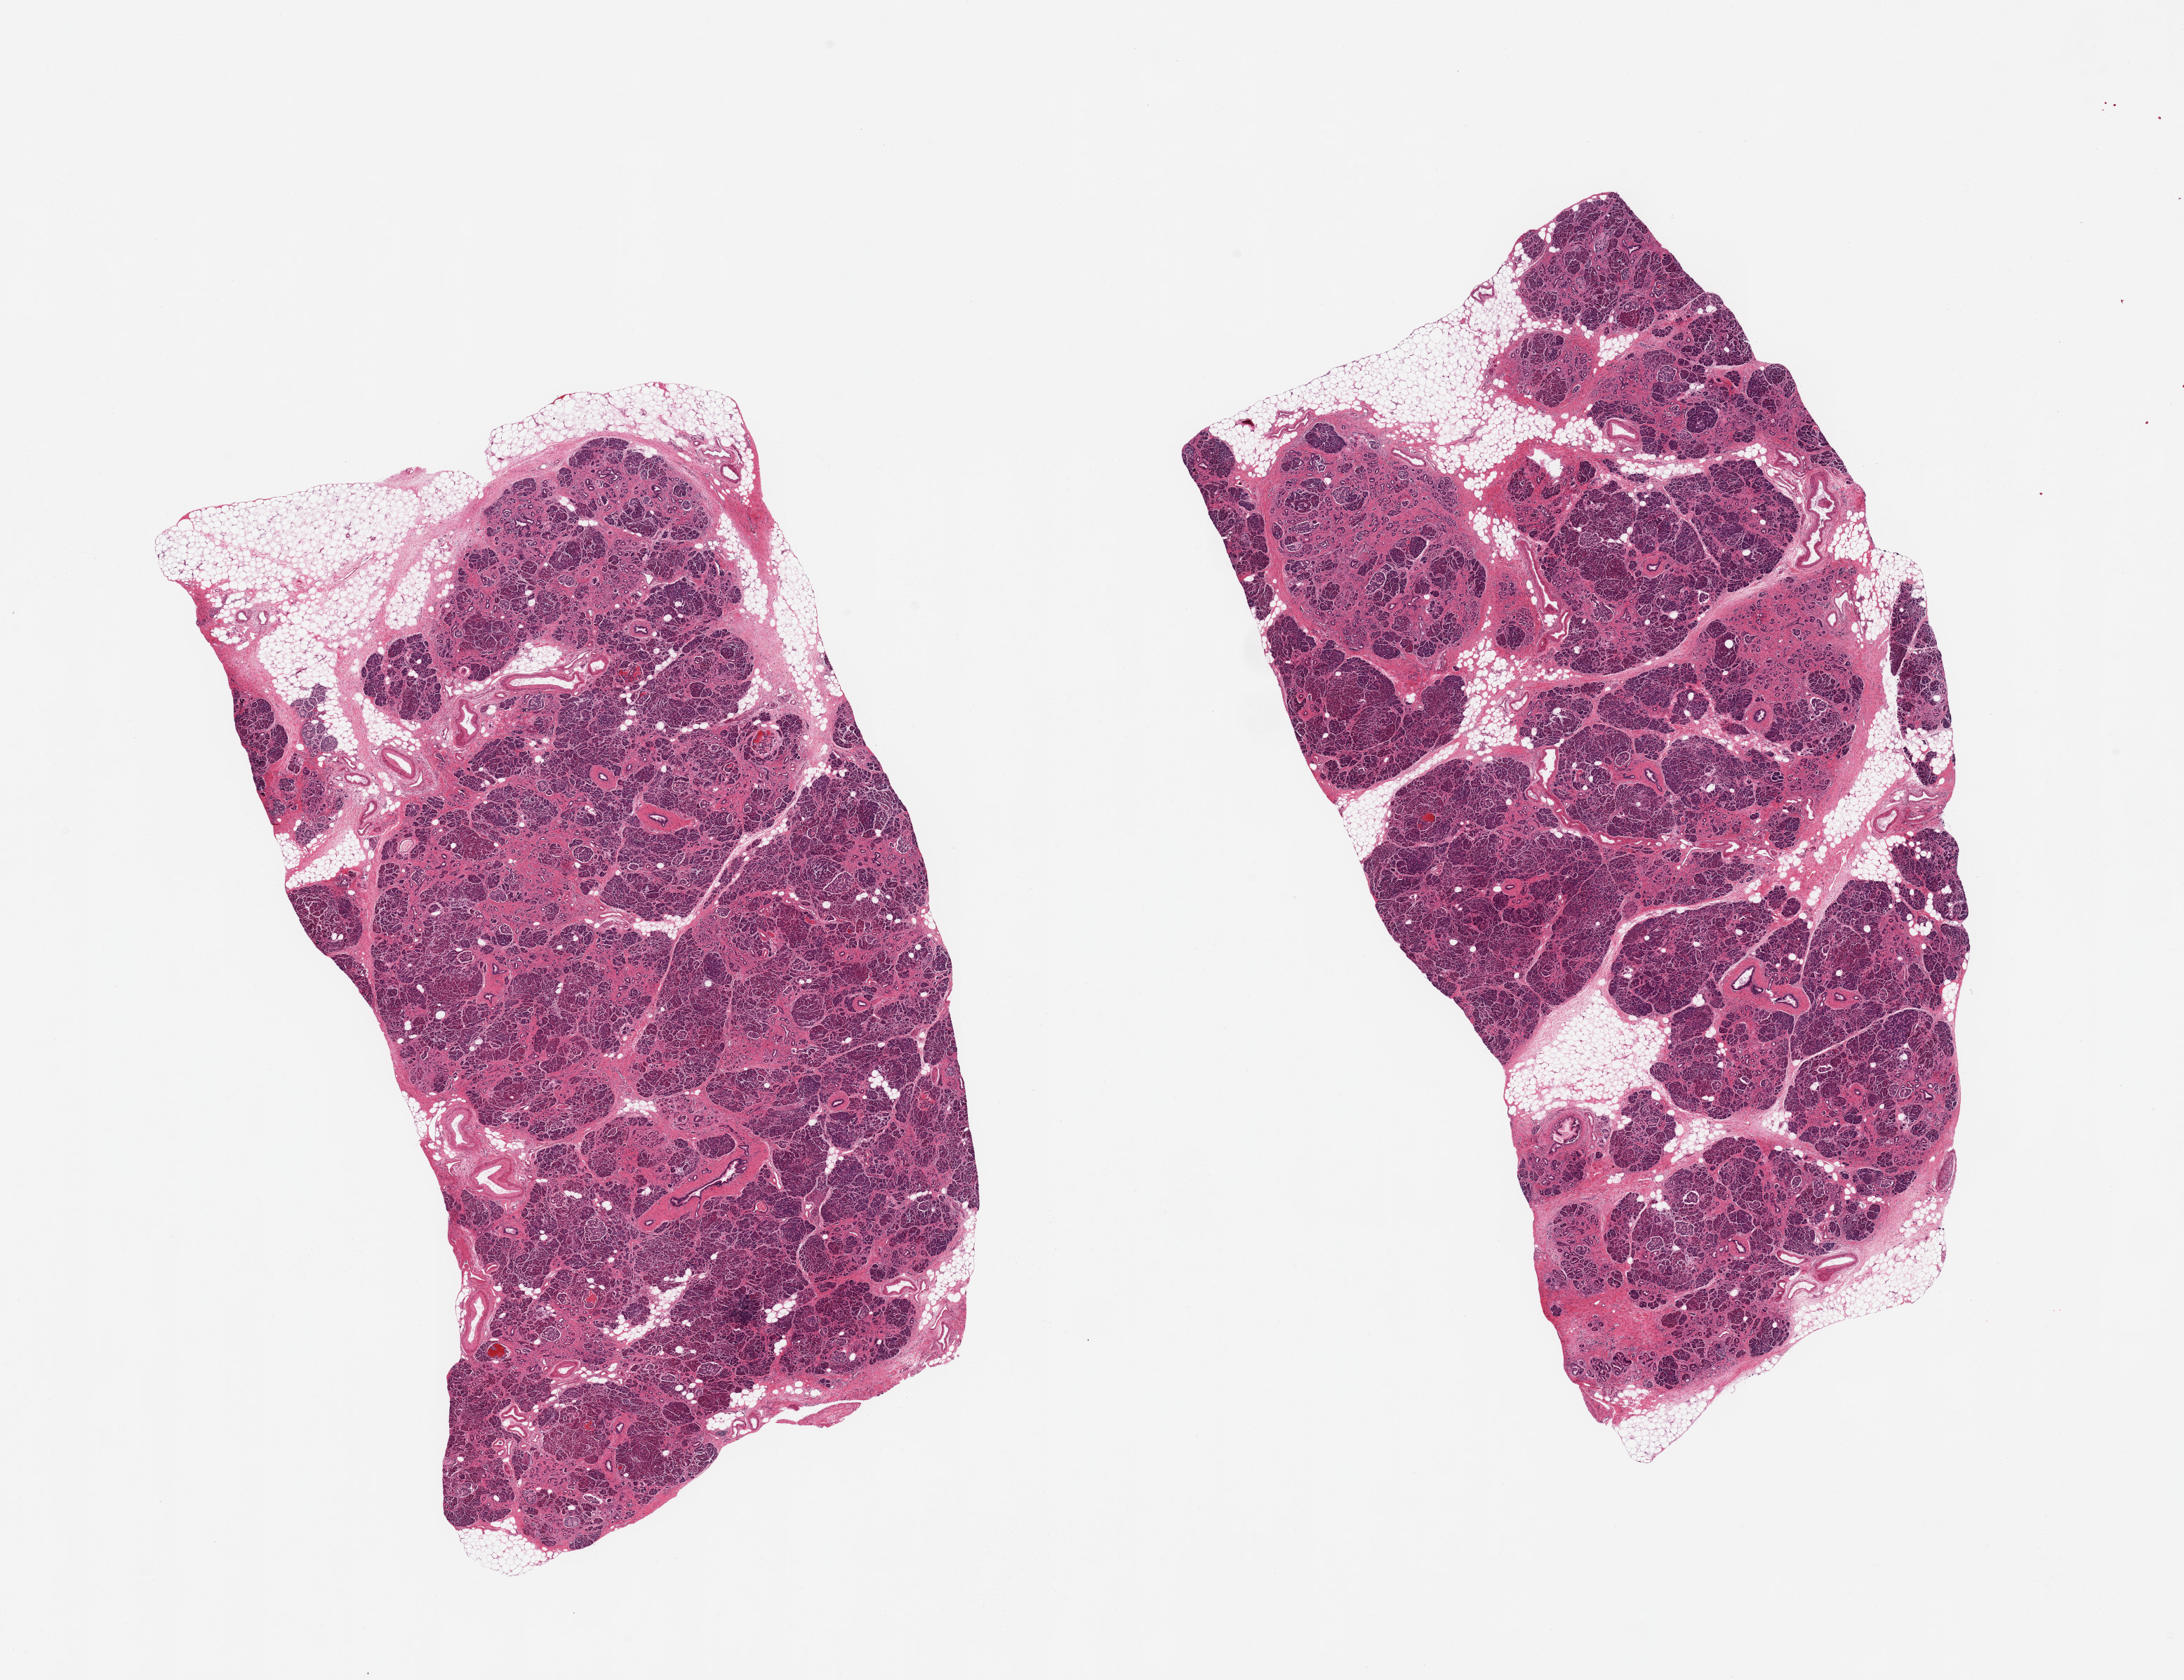
Haematoxylin and eosin whole-slide image — shown as a low-resolution overview of the whole scanned area (about 24.6 x 18.9 mm). Male donor.
Specimen: PAXgene-fixed, paraffin-embedded tissue; sampled site (target tissue): pancreas; tissue donor sample.